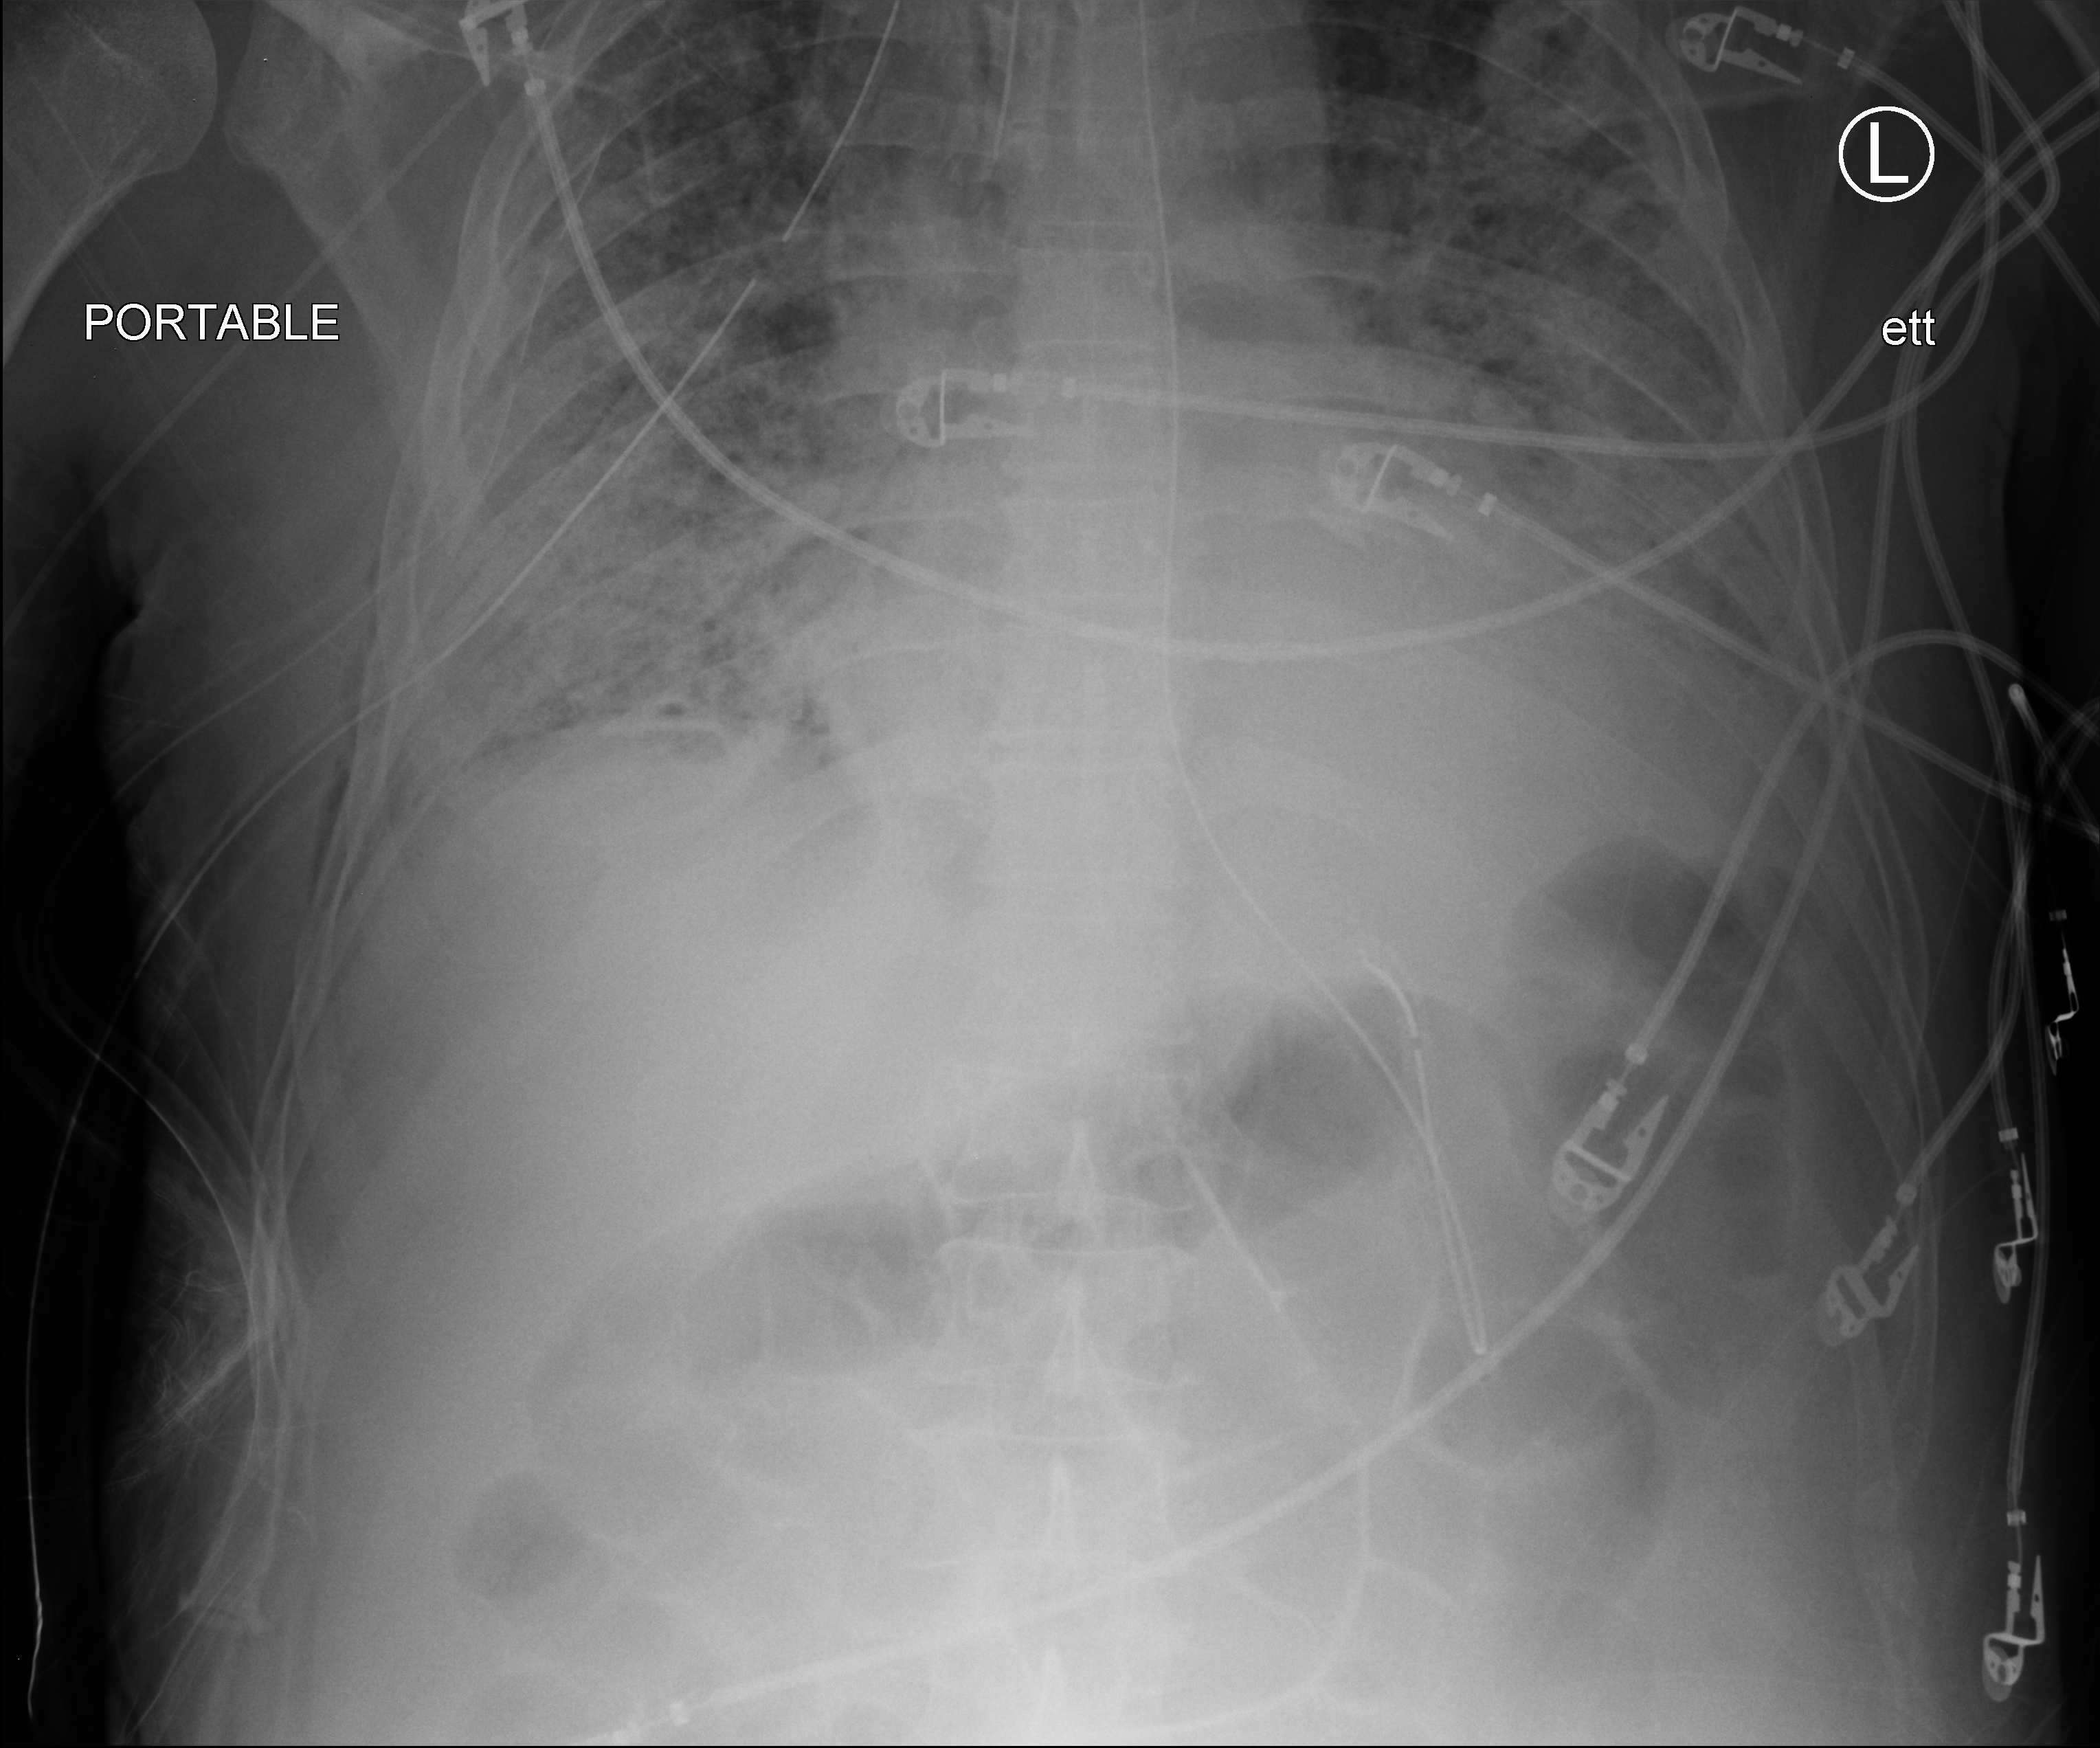
Chest X-ray (portable), anteroposterior (AP) projection. Patient hospitalised with COVID-19; male, aged 60–74 years.
Admission-level facts for this patient (not findings on this image; timing relative to this image not recorded): smoking status (admission record): never; admitted to intensive care during this hospital stay: yes; chronic kidney disease (admission record): no.